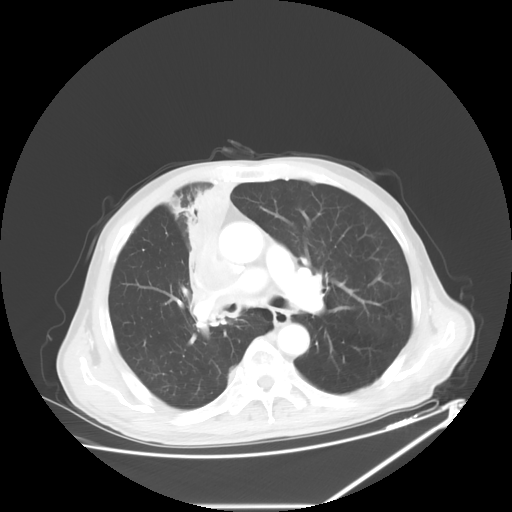
Chest CT, one axial slice; slice 38 of 60 in the series (ordered by position); lung window (W 1500 / L -600 HU); 512 × 512 image matrix, field of view 410 × 410 mm. Male patient, age 73 years. From the clinical record (not read from this slice): clinical TNM (as recorded): T2a N1 M0.
Structures marked on this image (bounding box drawn by a radiologist):
- lung tumour (recorded histology: squamous cell carcinoma): bounding box <173,186,238,327> (left, top, right, bottom; pixels)